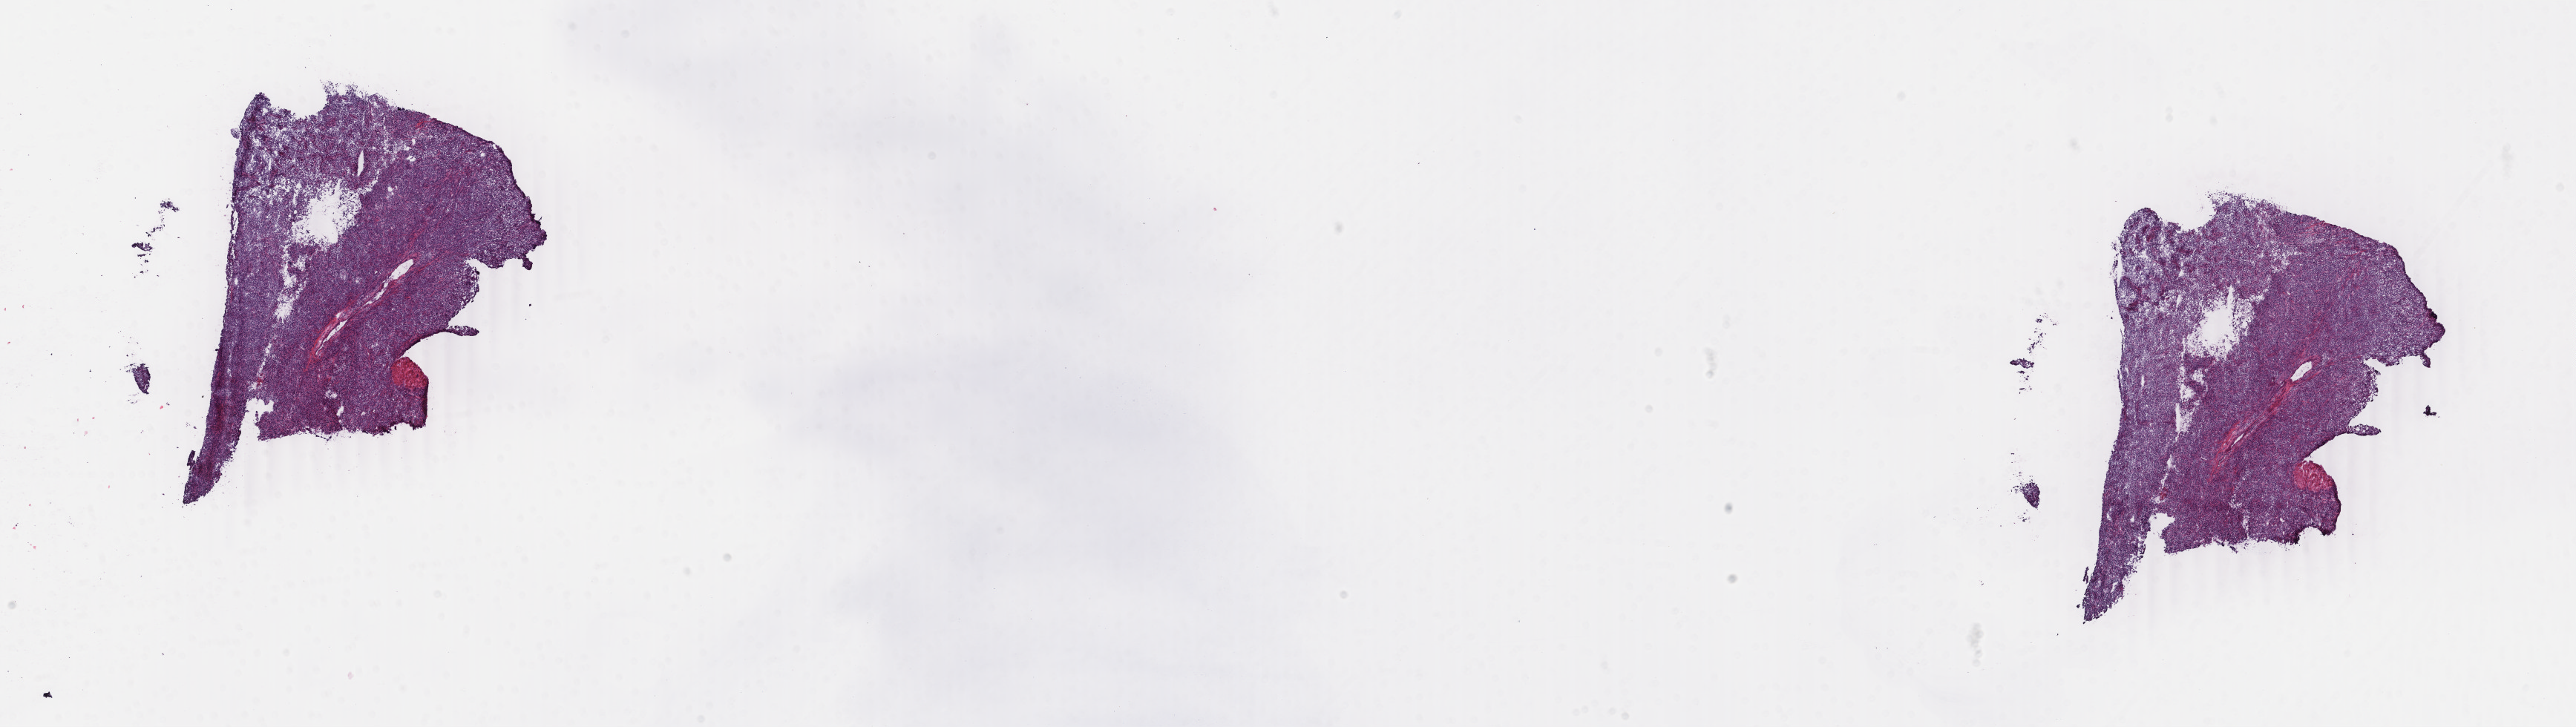
Digitized Hematoxylin and eosin (H&E) stained tissue section (whole slide), whole scanned area (about 27.6 x 7.8 mm, from a 40x scan) shown as a low-resolution overview, frozen section from the bottom of the tissue portion, primary tumour sample from the bladder. Female, age 57 years at initial diagnosis. Histologic grade: high grade. Slide review estimates, as recorded: tumour cells 85%, tumour nuclei 90%, normal cells 0%, stromal cells 3%, necrosis 12%. Inflammatory infiltration, as recorded: lymphocyte infiltration 3%, monocyte infiltration 0%, neutrophil infiltration 0%.
Lymph nodes positive (case pathology): 0 of 12 examined. Diagnosis: Transitional cell carcinoma. AJCC pathologic stage: III.